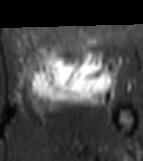
MRI of an extremity soft-tissue mass, one axial slice; position 36 of 81 along the scan axis; STIR; MR volume resampled by the dataset authors to the PET/CT grid (not the native acquisition matrix); 143 × 161 image matrix. Female patient. Case-level facts recorded for this patient, not image findings: histological type: myxofibrosarcoma; grade: intermediate; site of the primary tumour: left thigh.
Structures marked on this image (expert contour drawn on MRI and transferred to this co-registered scan by the dataset authors):
- gross tumour volume including surrounding oedema: bounding box [x1, y1, x2, y2] px = [26, 46, 118, 116]
- gross tumour volume (mass): [31, 46, 111, 100]